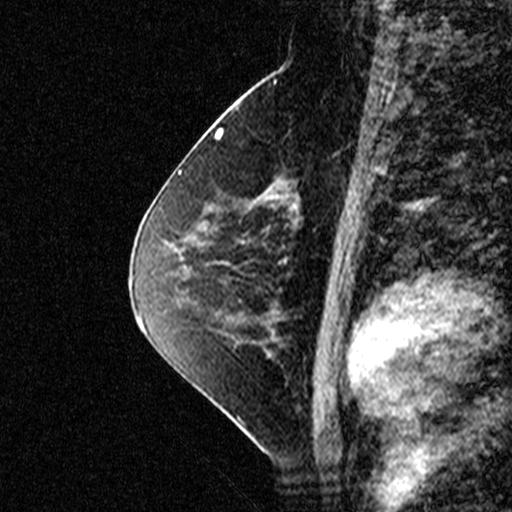
Breast MRI (dynamic contrast-enhanced), one sagittal slice. Slice 20 of 44 in the series (ordered by position). Dynamic contrast-enhanced study with each time point stored as its own series, time point 2 of 3 at this slice position (early post-contrast, ordered by acquisition time). 1.5 T. TE 4.5 ms, TR 11 ms. 512 × 512 image matrix, field of view 200 × 200 mm. Female patient, age 49 years. Case-level facts recorded for this patient, not image findings: setting: breast cancer imaged before/during neoadjuvant chemotherapy; receptor status: triple-negative.
Annotated regions visible in this slice (semi-automatically segmented with operator editing):
- analysis volume of interest (the breast-tissue region the enhancement analysis was run in; not a lesion): bounding box (x1, y1, x2, y2) in pixels: (254, 112, 347, 207)
- tumour enhancement mask (voxels above the 90 % enhancement threshold inside the analysis volume of interest): (276, 163, 347, 207)